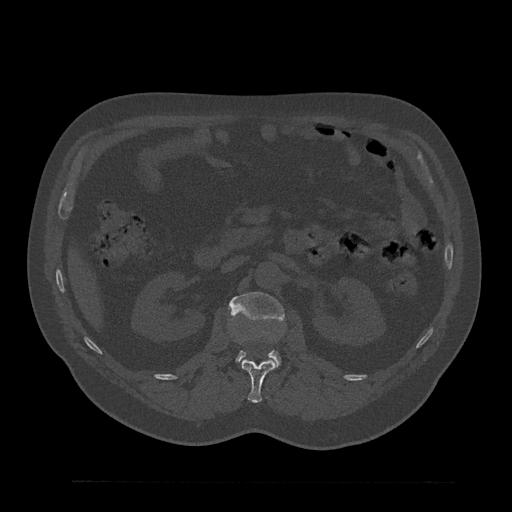
CT including the spine, one axial slice; slice 136 of 797 in the series (ordered by position); bone window (W 1800 / L 400 HU); 512 × 512 image matrix, field of view 430 × 430 mm. Patient: male, 61 years. From the clinical record (not read from this slice): primary cancer: prostate.
Structures marked on this image (semi-automatically segmented with operator editing):
- L1 vertebra: bounding box (x1, y1, x2, y2) in pixels: (241, 360, 276, 403)
- L2 vertebra: (228, 292, 284, 365)